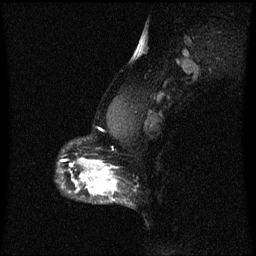
Breast MRI (dynamic contrast-enhanced), one sagittal slice; position 45 of 60 along the scan axis; dynamic contrast-enhanced series, image 2 of 3 at this slice position (ordered by acquisition); 1.5 T; TE 4.2 ms, TR 8.4 ms; 2 mm slice thickness; 256 × 256 image matrix. Patient: female, 40 years.
Outlined on this slice (semi-automatically segmented with operator editing):
- analysis volume of interest (the breast-tissue region the enhancement analysis was run in; not a lesion): box from (x=76, y=172) to (x=123, y=205) px
- tumour enhancement mask (voxels above the 70 % enhancement threshold inside the analysis volume of interest): (x=82, y=172)–(x=118, y=195)